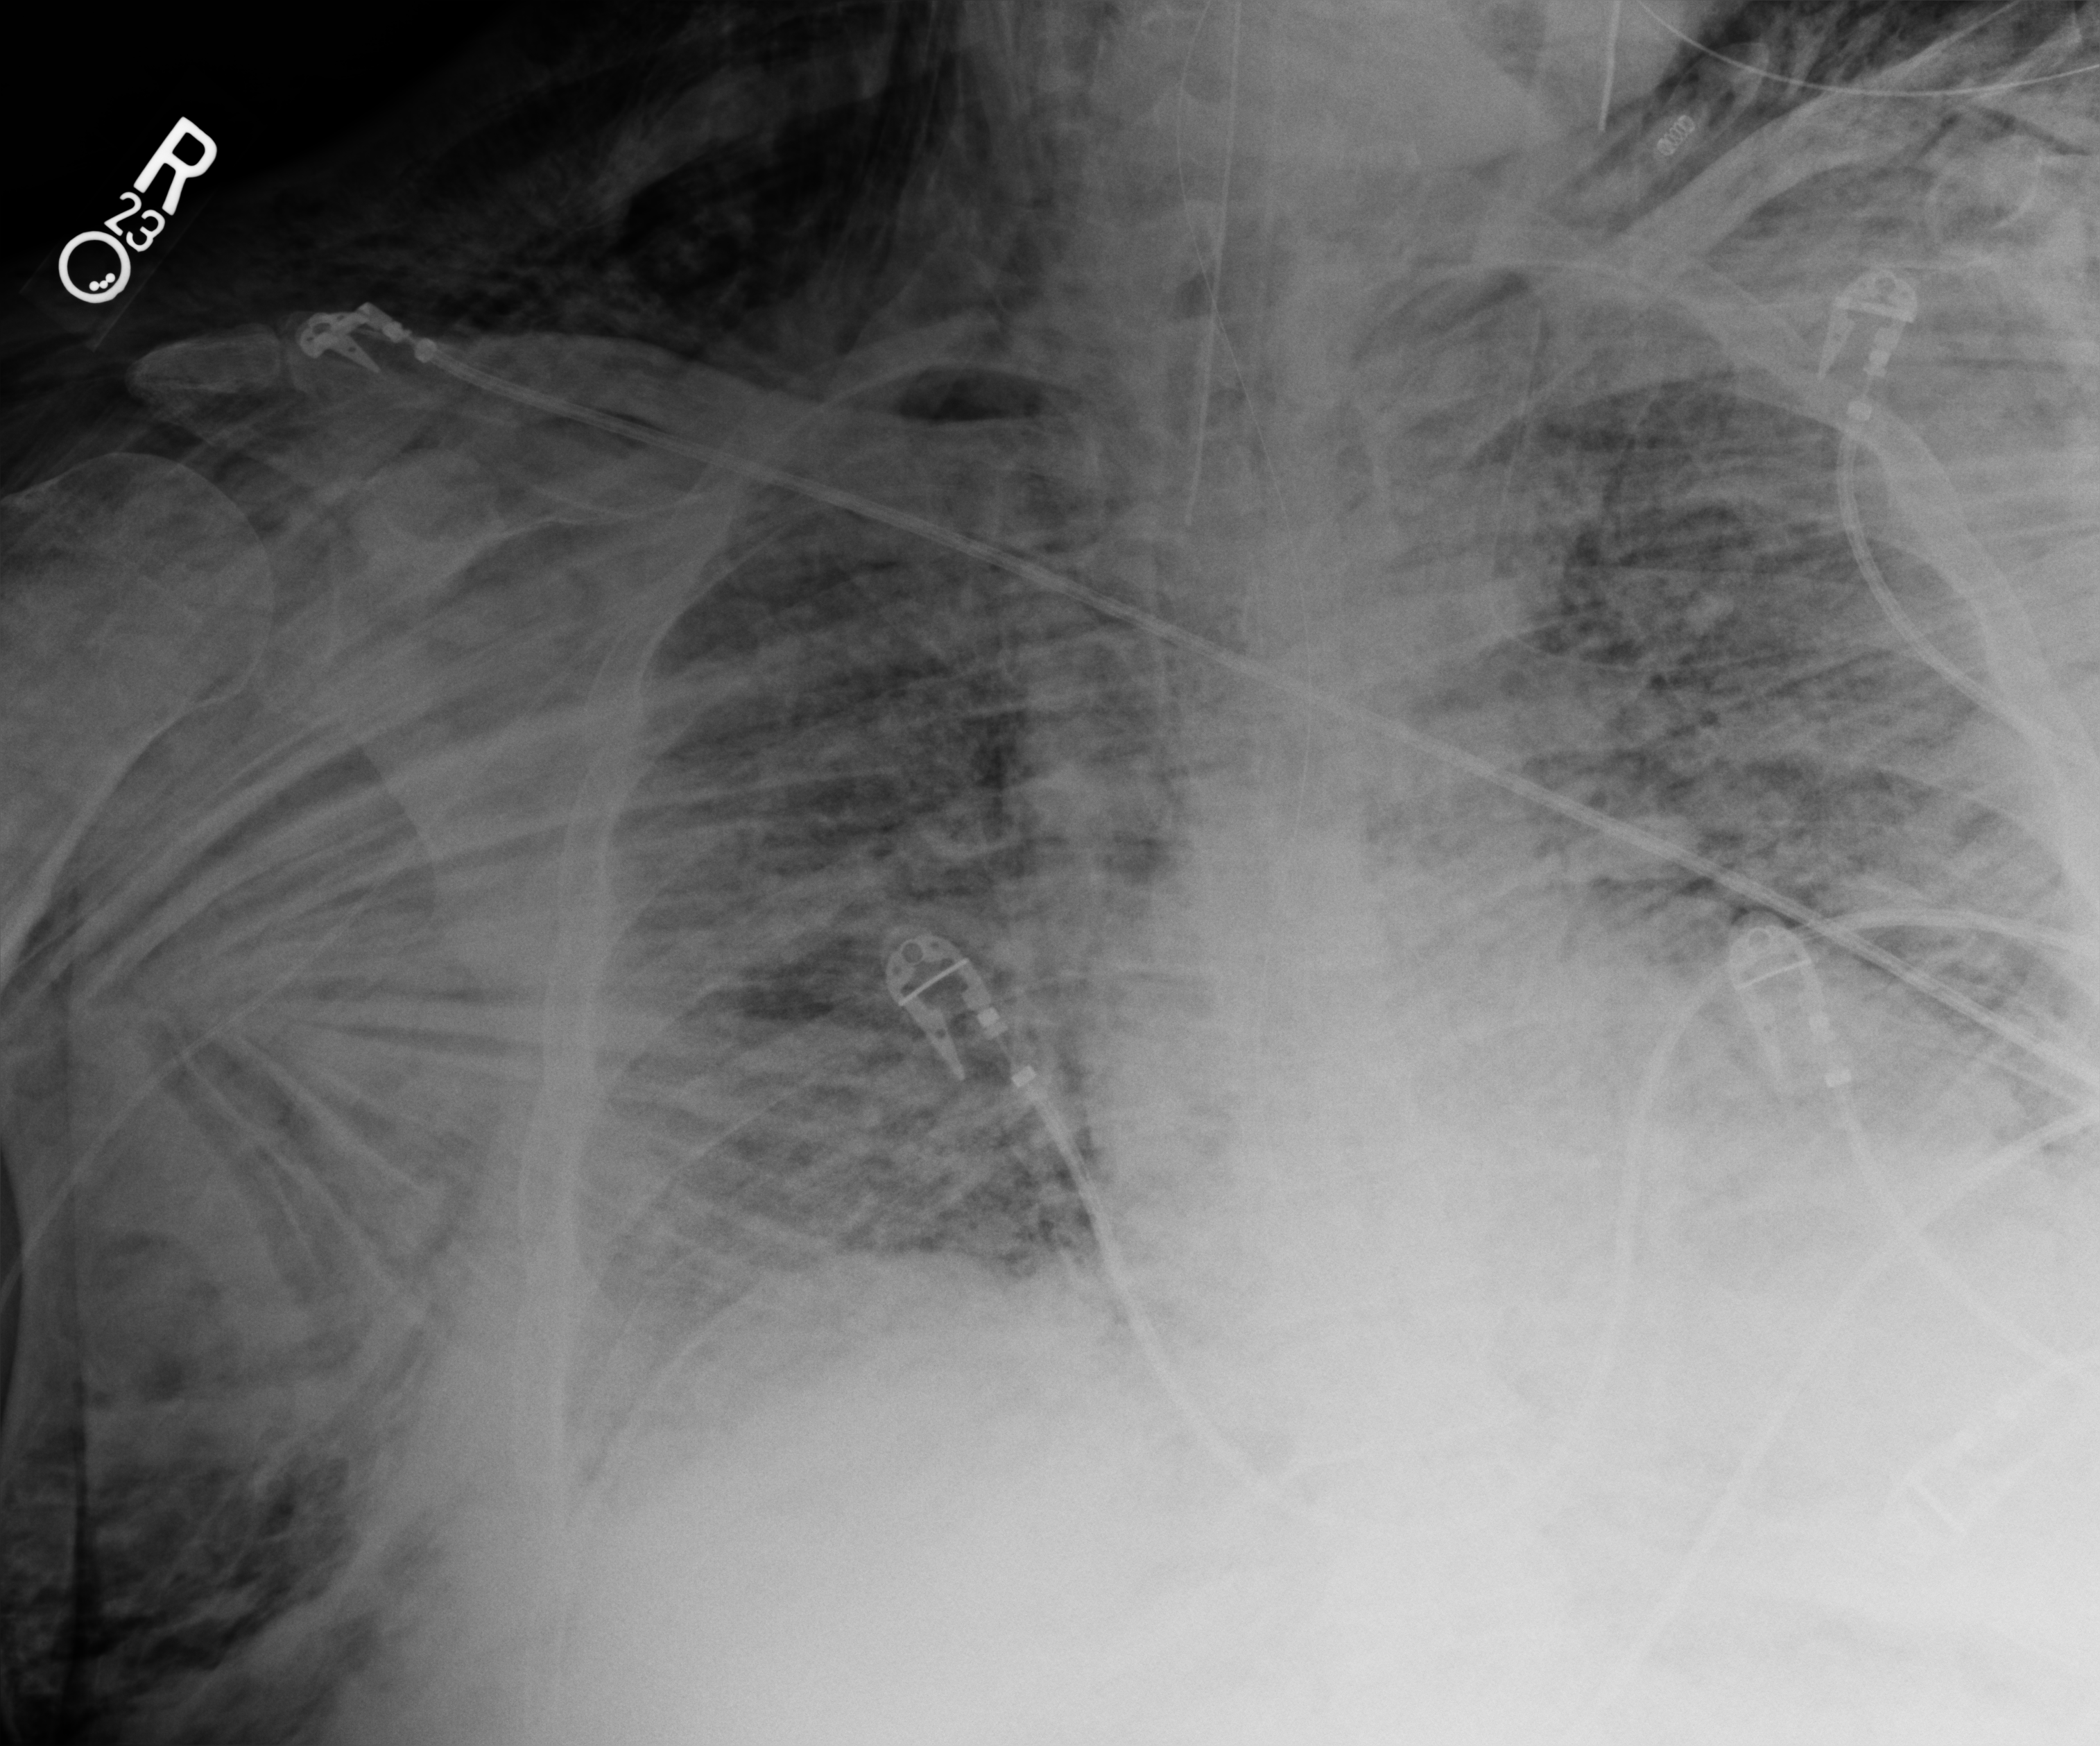
Portable chest radiograph; anteroposterior (AP) projection. Patient hospitalised with COVID-19, aged 18–59 years.
Admission-level facts for this patient (not findings on this image; timing relative to this image not recorded): mechanically ventilated during this hospital stay: yes.